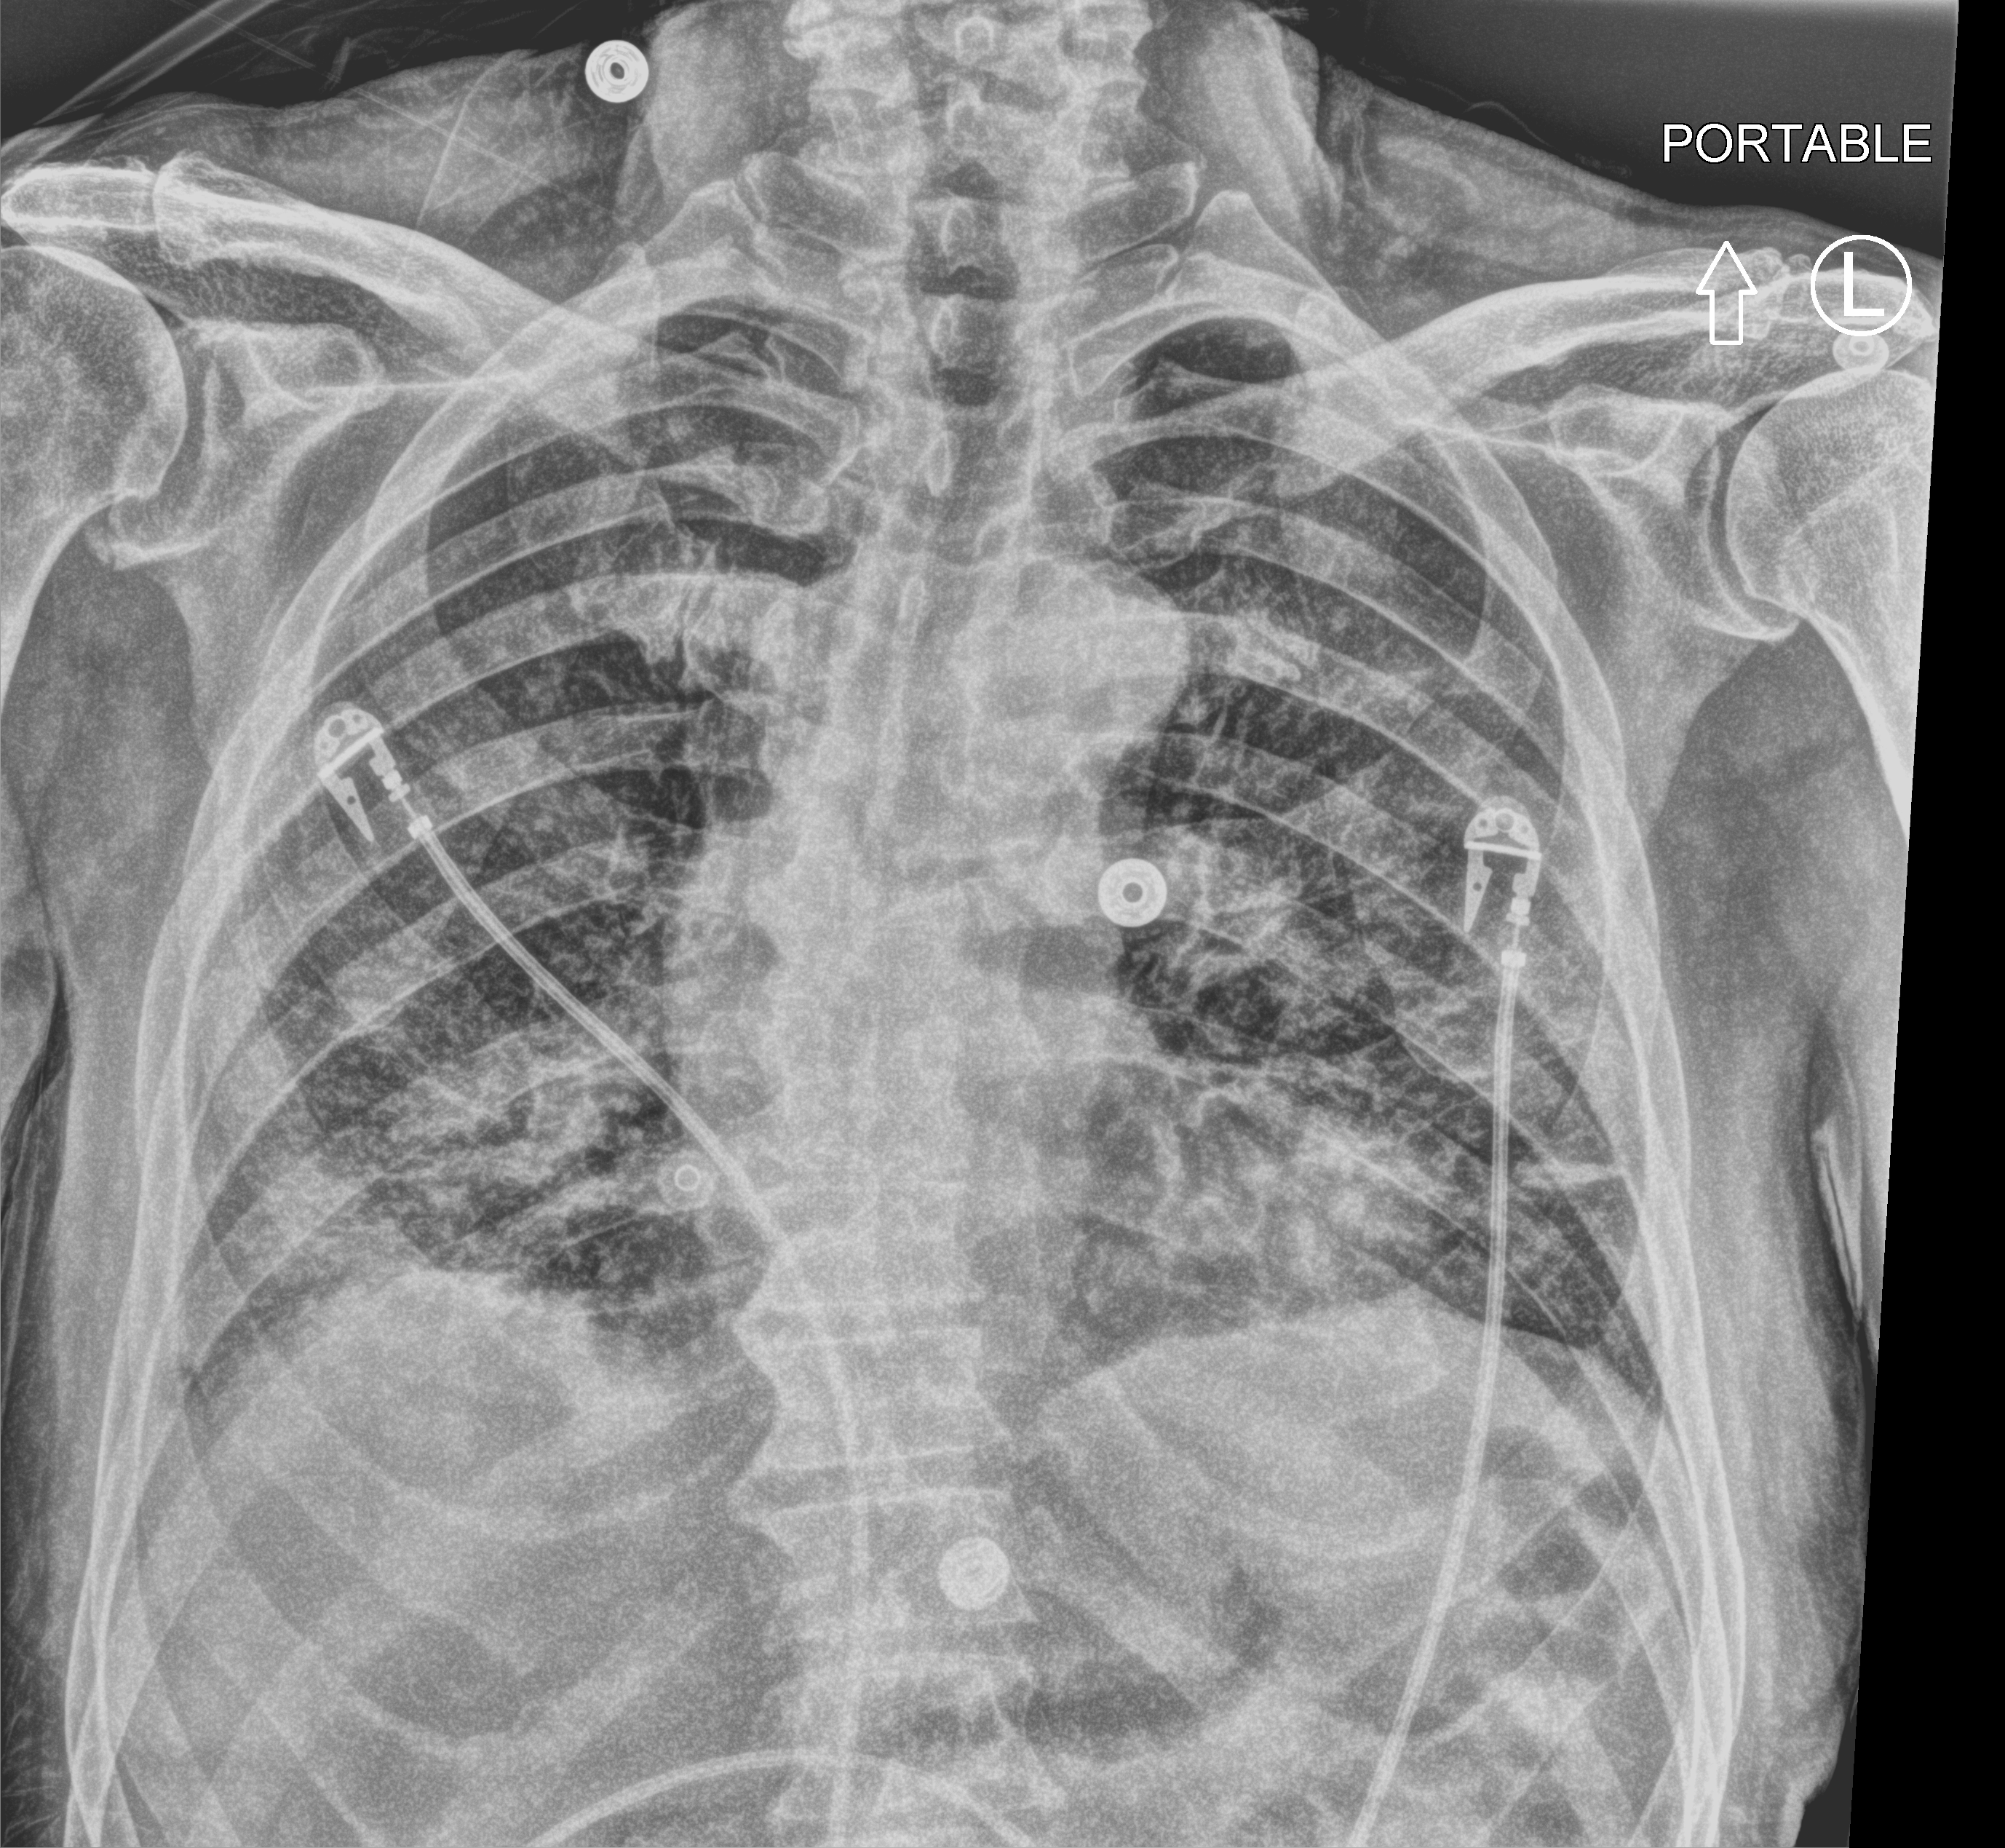
Chest X-ray (portable), anteroposterior (AP) projection. Male patient hospitalised with COVID-19, age 75–90 years.
From the hospital-stay record, not from the radiograph (when in the stay this image was taken is not recorded): mechanically ventilated during this hospital stay: no.